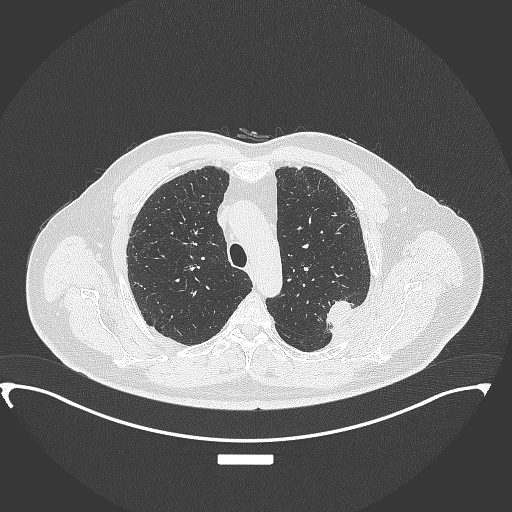
Chest CT, one axial slice. Position 272 of 350 along the scan axis. Reconstruction kernel B70f. 120 kVp. Lung window (W 1500 / L -600 HU). 1 mm slice thickness. 512 × 512 image matrix, field of view 459 × 459 mm. Male patient, age 64 years. Case-level facts recorded for this patient, not image findings: clinical TNM (as recorded): T1c N1 M1.
Outlined on this slice (bounding box drawn by a radiologist):
- lung tumour (recorded histology: adenocarcinoma): bounding box [x1, y1, x2, y2] px = [321, 296, 363, 337]